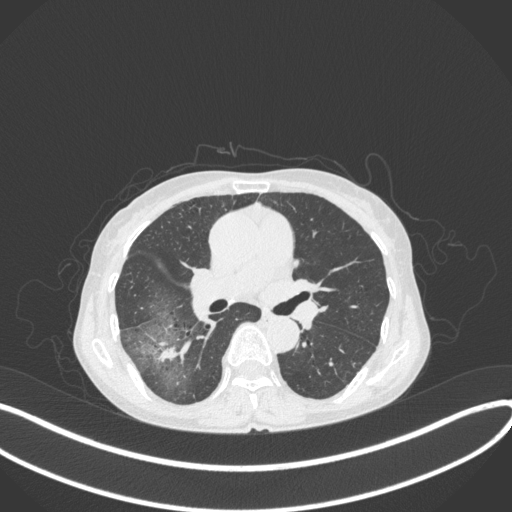
Chest CT, one axial slice. Slice 224 of 379 in the series (ordered by position). 120 kVp. Lung window (W 1500 / L -600 HU). 1 mm slice thickness. 512 × 512 image matrix, field of view 400 × 400 mm. Patient: female, 69 years. Case-level facts recorded for this patient, not image findings: clinical TNM (as recorded): T1b N0 M0; histopathological grade: G2-3.
Outlined on this slice (bounding box drawn by a radiologist):
- lung tumour (recorded histology: adenocarcinoma): bounding box (x1, y1, x2, y2) in pixels: (155, 336, 193, 371)